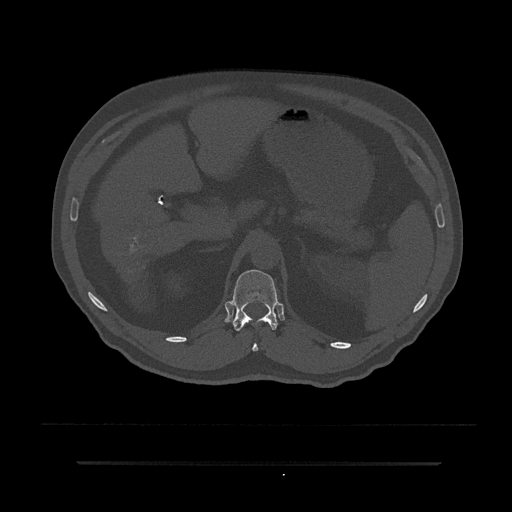
CT including the spine, one axial slice. Slice 217 of 797 in the series (ordered by position). 120 kVp. Bone window (W 1800 / L 400 HU). 0.5 mm slice thickness. 512 × 512 image matrix, field of view 464 × 464 mm. Male patient, age 59 years. From the clinical record (not read from this slice): primary cancer: bile ducts; vertebrae with lytic lesions (as recorded): T10.
Structures marked on this image (semi-automatic segmentation, software-assisted and operator-edited):
- T12 vertebra: bounding box <232,269,279,351> (left, top, right, bottom; pixels)